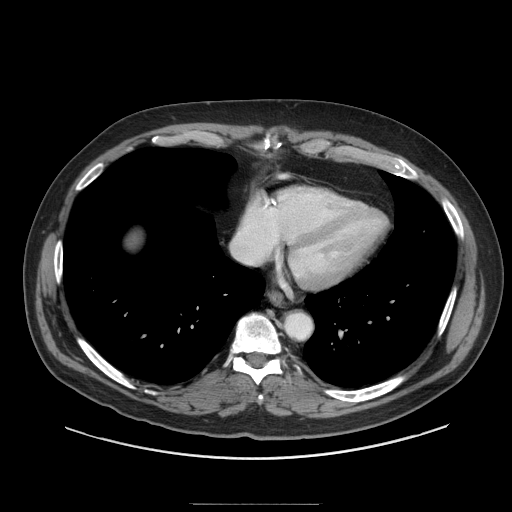
Contrast-enhanced abdominal CT (liver protocol), one axial slice. Position 87 of 91 along the scan axis. Reconstruction kernel STANDARD. Soft-tissue window (W 400 / L 40 HU). 512 × 512 image matrix, field of view 440 × 440 mm. Case-level facts recorded for this patient, not image findings: diagnosis: hepatocellular carcinoma (patient treated with transarterial chemoembolisation; whether this scan precedes or follows treatment is not stated here); TNM stage (as recorded): Stage-I; Child-Pugh class: A; tumour differentiation: well differentiated; tumour size: 4 cm.
Structures marked on this image (semi-automatic segmentation, software-assisted and operator-edited):
- liver parenchyma outside the tumour (the mass and vessels are separate outlines, so this box may not span the whole liver): bounding box (x1, y1, x2, y2) in pixels: (128, 234, 138, 246)